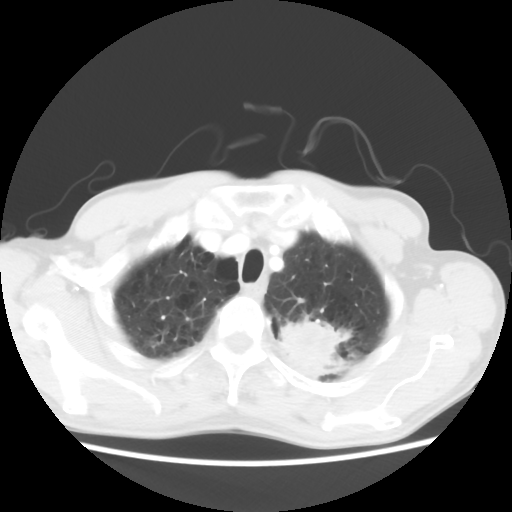
Chest CT, one axial slice; slice 55 of 64 in the series (ordered by position); reconstruction kernel STANDARD; 120 kVp; lung window (W 1500 / L -600 HU); 512 × 512 image matrix, field of view 346 × 346 mm. Male patient, age 63 years. From the clinical record (not read from this slice): clinical TNM (as recorded): T2 N0 M0.
Outlined on this slice (bounding box drawn by a radiologist):
- lung tumour (recorded histology: adenocarcinoma): box from (x=278, y=314) to (x=351, y=382) px